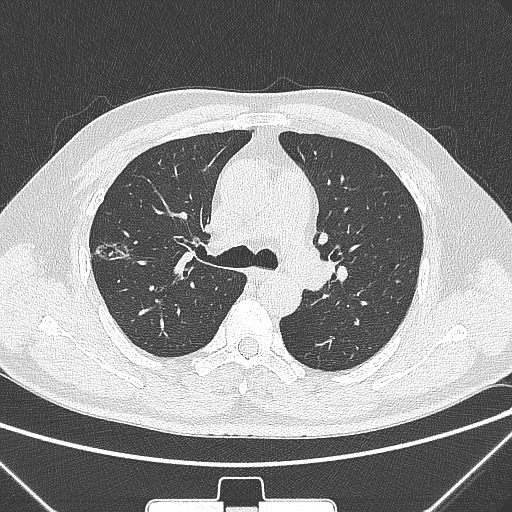
Chest CT, one axial slice; position 200 of 320 along the scan axis; lung window (W 1500 / L -600 HU); 512 × 512 image matrix, field of view 350 × 350 mm. Male patient, age 58 years. From the clinical record (not read from this slice): clinical TNM (as recorded): T1c N0 M0.
Outlined on this slice (rectangle marked by the reading radiologist):
- lung tumour (recorded histology: adenocarcinoma): bounding box (x1, y1, x2, y2) in pixels: (89, 232, 139, 273)